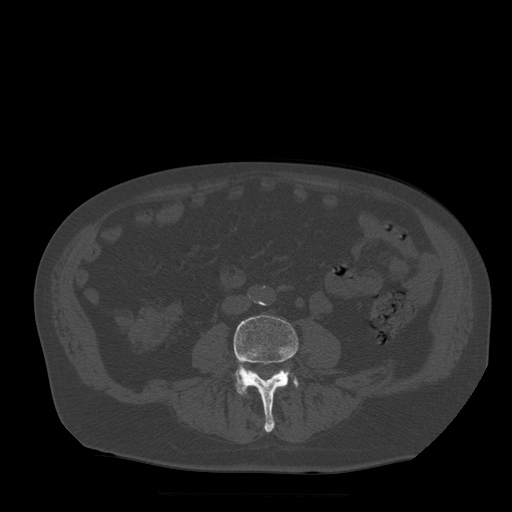
CT including the spine, one axial slice. Slice 113 of 522 in the series (ordered by position). Bone window (W 1800 / L 400 HU). 1.25 mm slice thickness. 512 × 512 image matrix. Patient age 72 years. Case-level facts recorded for this patient, not image findings: primary cancer: prostate.
Structures marked on this image (semi-automatic segmentation, software-assisted and operator-edited):
- L3 vertebra: bounding box <251,385,278,388> (left, top, right, bottom; pixels)
- L4 vertebra: <234,315,298,433>
- L5 vertebra: <234,369,299,394>